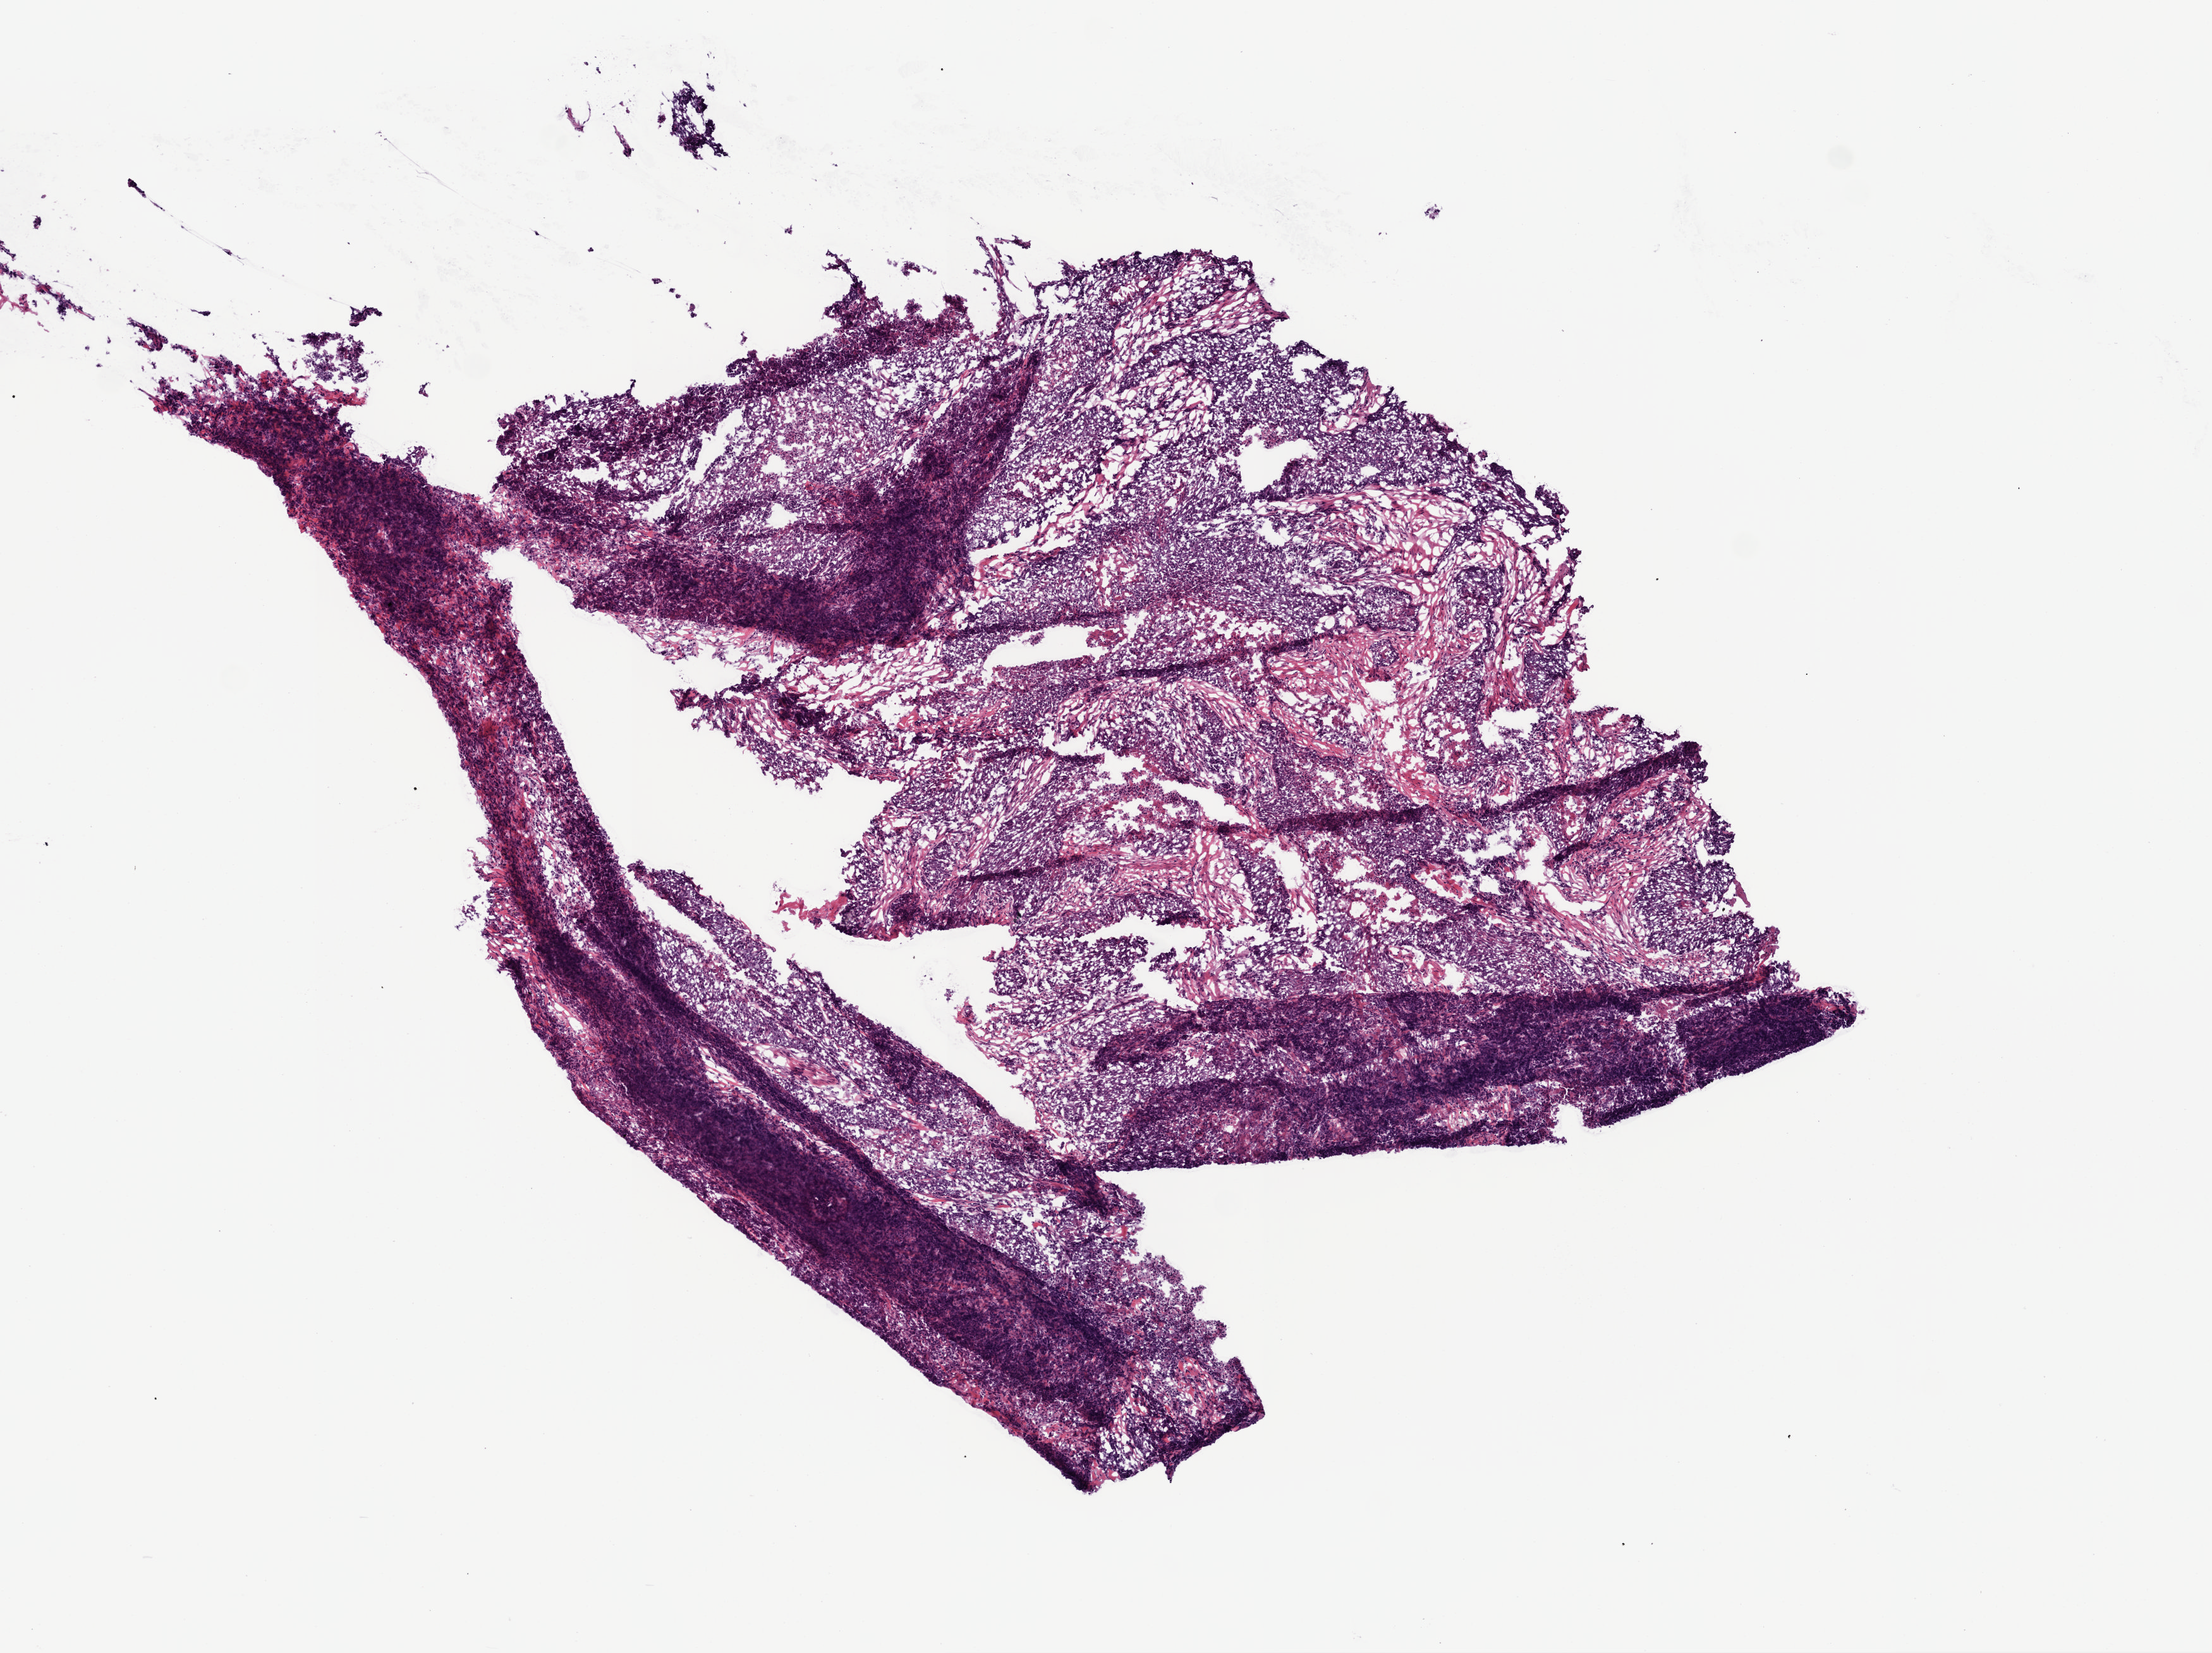
Hematoxylin and eosin (H&E) stained whole-slide image, shown as a low-resolution overview of the whole scanned area (about 7.0 x 5.2 mm), frozen section from the top of the tissue portion, primary tumour sample from the head and neck. Male patient; age at initial diagnosis 63 years. Histologic grade: G3 (poorly differentiated). Composition of this section per pathologist review: tumour cells 75%, tumour nuclei 85%, normal cells 0%, stromal cells 15%, necrosis 10%.
AJCC pathologic stage: III (7th edition). TNM: T3 N0. Diagnosis: Squamous cell carcinoma, NOS.